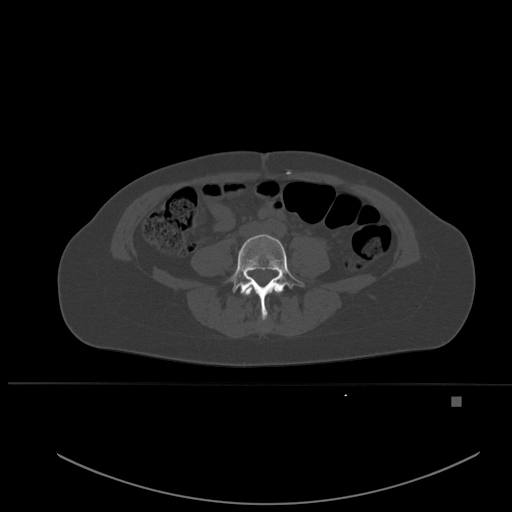
CT including the spine, one axial slice; position 175 of 651 along the scan axis; bone window (W 1800 / L 400 HU); 1.5 mm slice thickness; 512 × 512 image matrix, field of view 443 × 443 mm. Patient: female, 49 years. Case-level facts recorded for this patient, not image findings: primary cancer: breast; vertebrae with lytic lesions (as recorded): L3, T12, L4.
Annotated regions visible in this slice (semi-automatic segmentation, software-assisted and operator-edited):
- L3 vertebra: bounding box (x1, y1, x2, y2) in pixels: (243, 287, 282, 296)
- L4 vertebra: (225, 234, 305, 319)